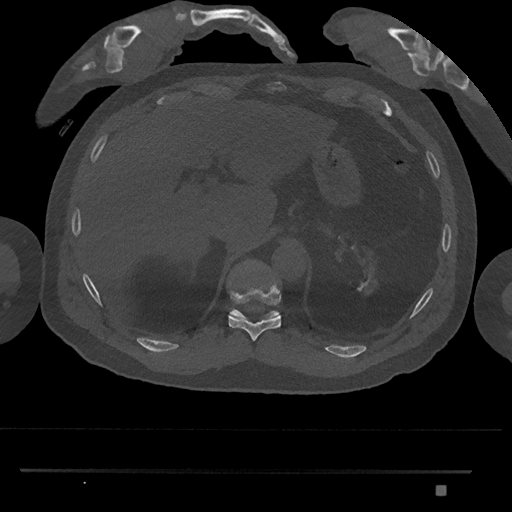
CT including the spine, one axial slice; position 988 of 1134 along the scan axis; reconstruction kernel Br40s/3; 120 kVp; bone window (W 1800 / L 400 HU); 512 × 512 image matrix, field of view 429 × 429 mm. Male patient, age 65 years. Case-level facts recorded for this patient, not image findings: primary cancer: prostate.
Outlined on this slice (semi-automatically segmented with operator editing):
- T10 vertebra: bounding box <228,273,281,341> (left, top, right, bottom; pixels)
- T11 vertebra: <230,308,280,319>